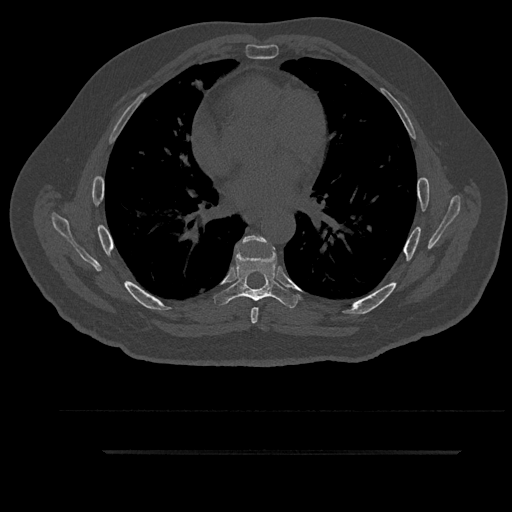
CT including the spine, one axial slice. Position 542 of 797 along the scan axis. 120 kVp. Bone window (W 1800 / L 400 HU). 512 × 512 image matrix, field of view 432 × 432 mm. Patient: male, 63 years. From the clinical record (not read from this slice): primary cancer: renal; vertebrae with lytic lesions (as recorded): T8.
Annotated regions visible in this slice (semi-automatically segmented with operator editing):
- T6 vertebra: bounding box <237,236,269,324> (left, top, right, bottom; pixels)
- T7 vertebra: <214,242,300,308>